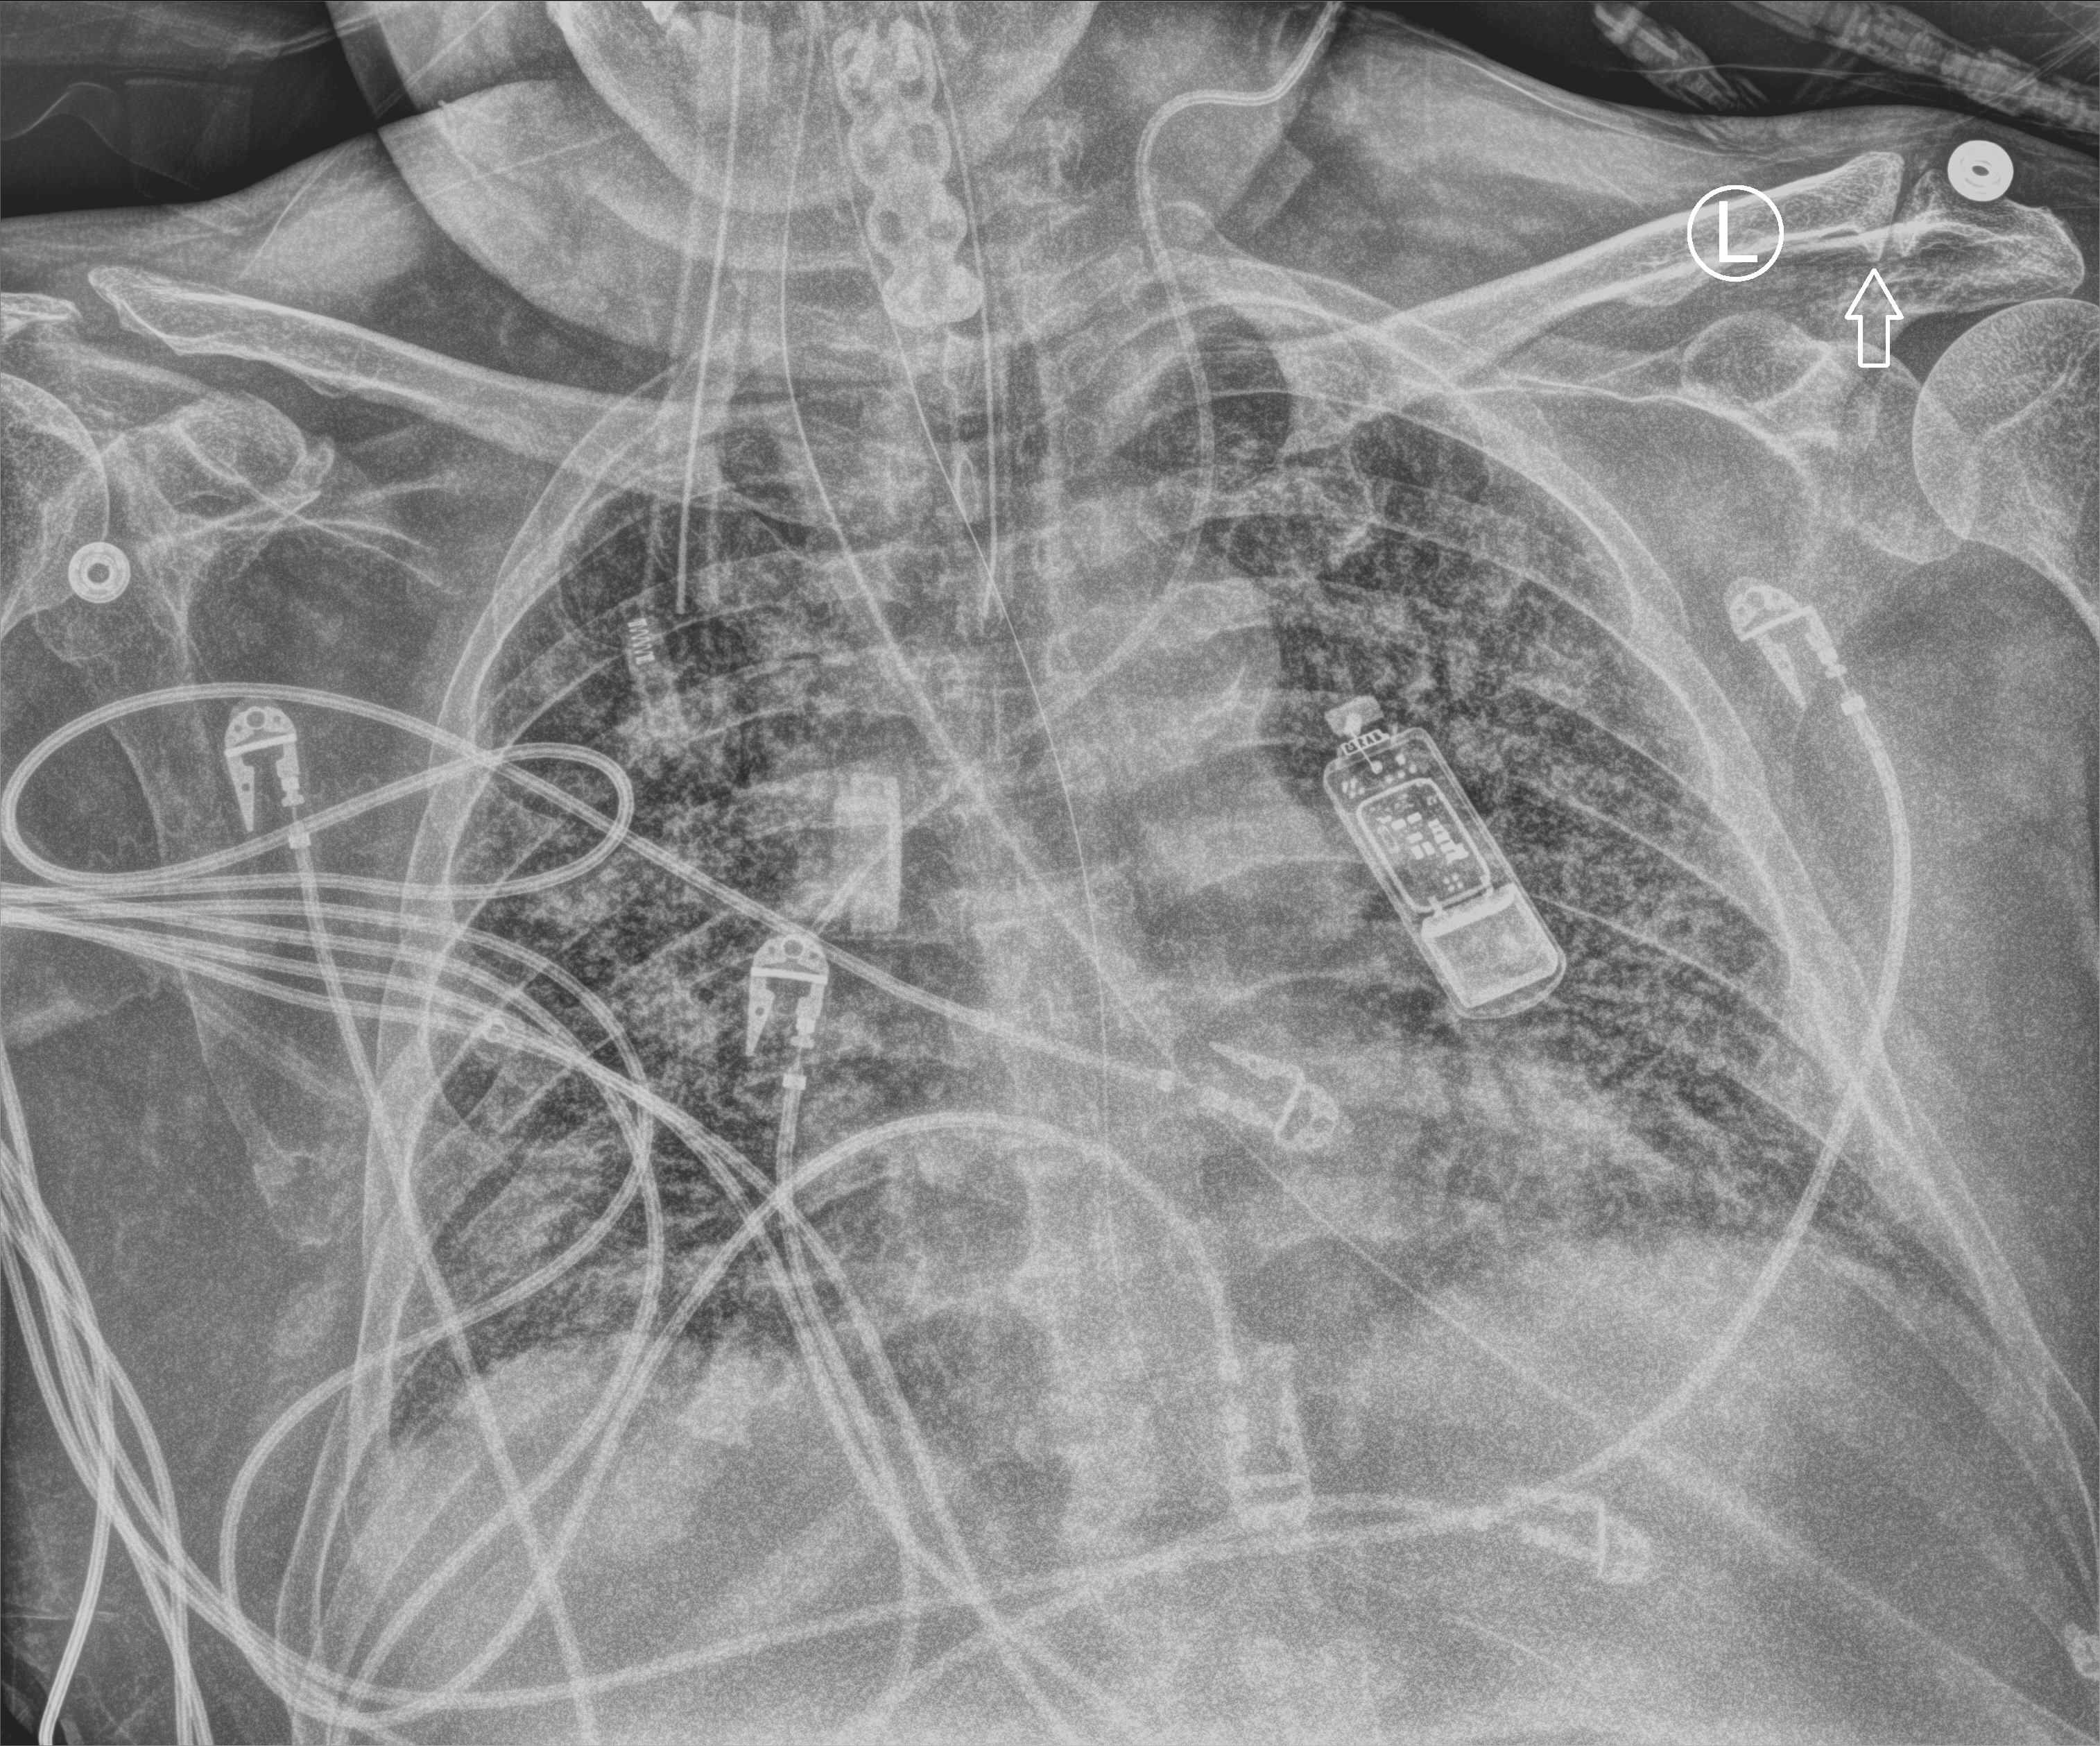
Portable chest radiograph; anteroposterior (AP) projection. Male patient hospitalised with COVID-19, age 60–74 years.
Hospital-stay facts (about this admission, not read from this image; timing relative to this image not recorded):
- length of hospital stay: 7 days